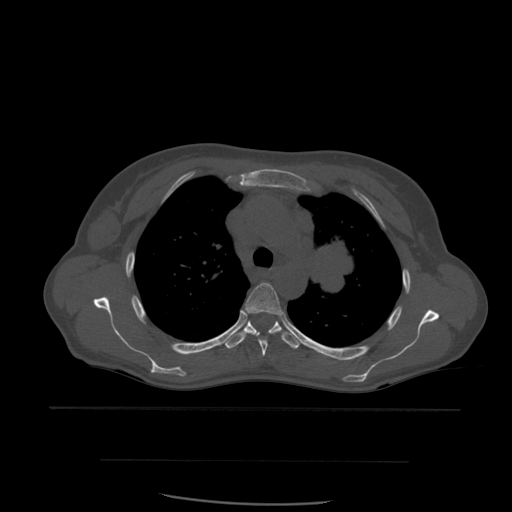
CT including the spine, one axial slice; slice 419 of 574 in the series (ordered by position); bone window (W 1800 / L 400 HU); 1.25 mm slice thickness; 512 × 512 image matrix, field of view 392 × 392 mm. Patient age 48 years. Case-level facts recorded for this patient, not image findings: primary cancer: lung; vertebrae with lytic lesions (as recorded): T11.
Outlined on this slice (semi-automatically segmented with operator editing):
- T4 vertebra: box from (x=243, y=283) to (x=284, y=357) px
- T5 vertebra: (x=225, y=321)–(x=300, y=349)